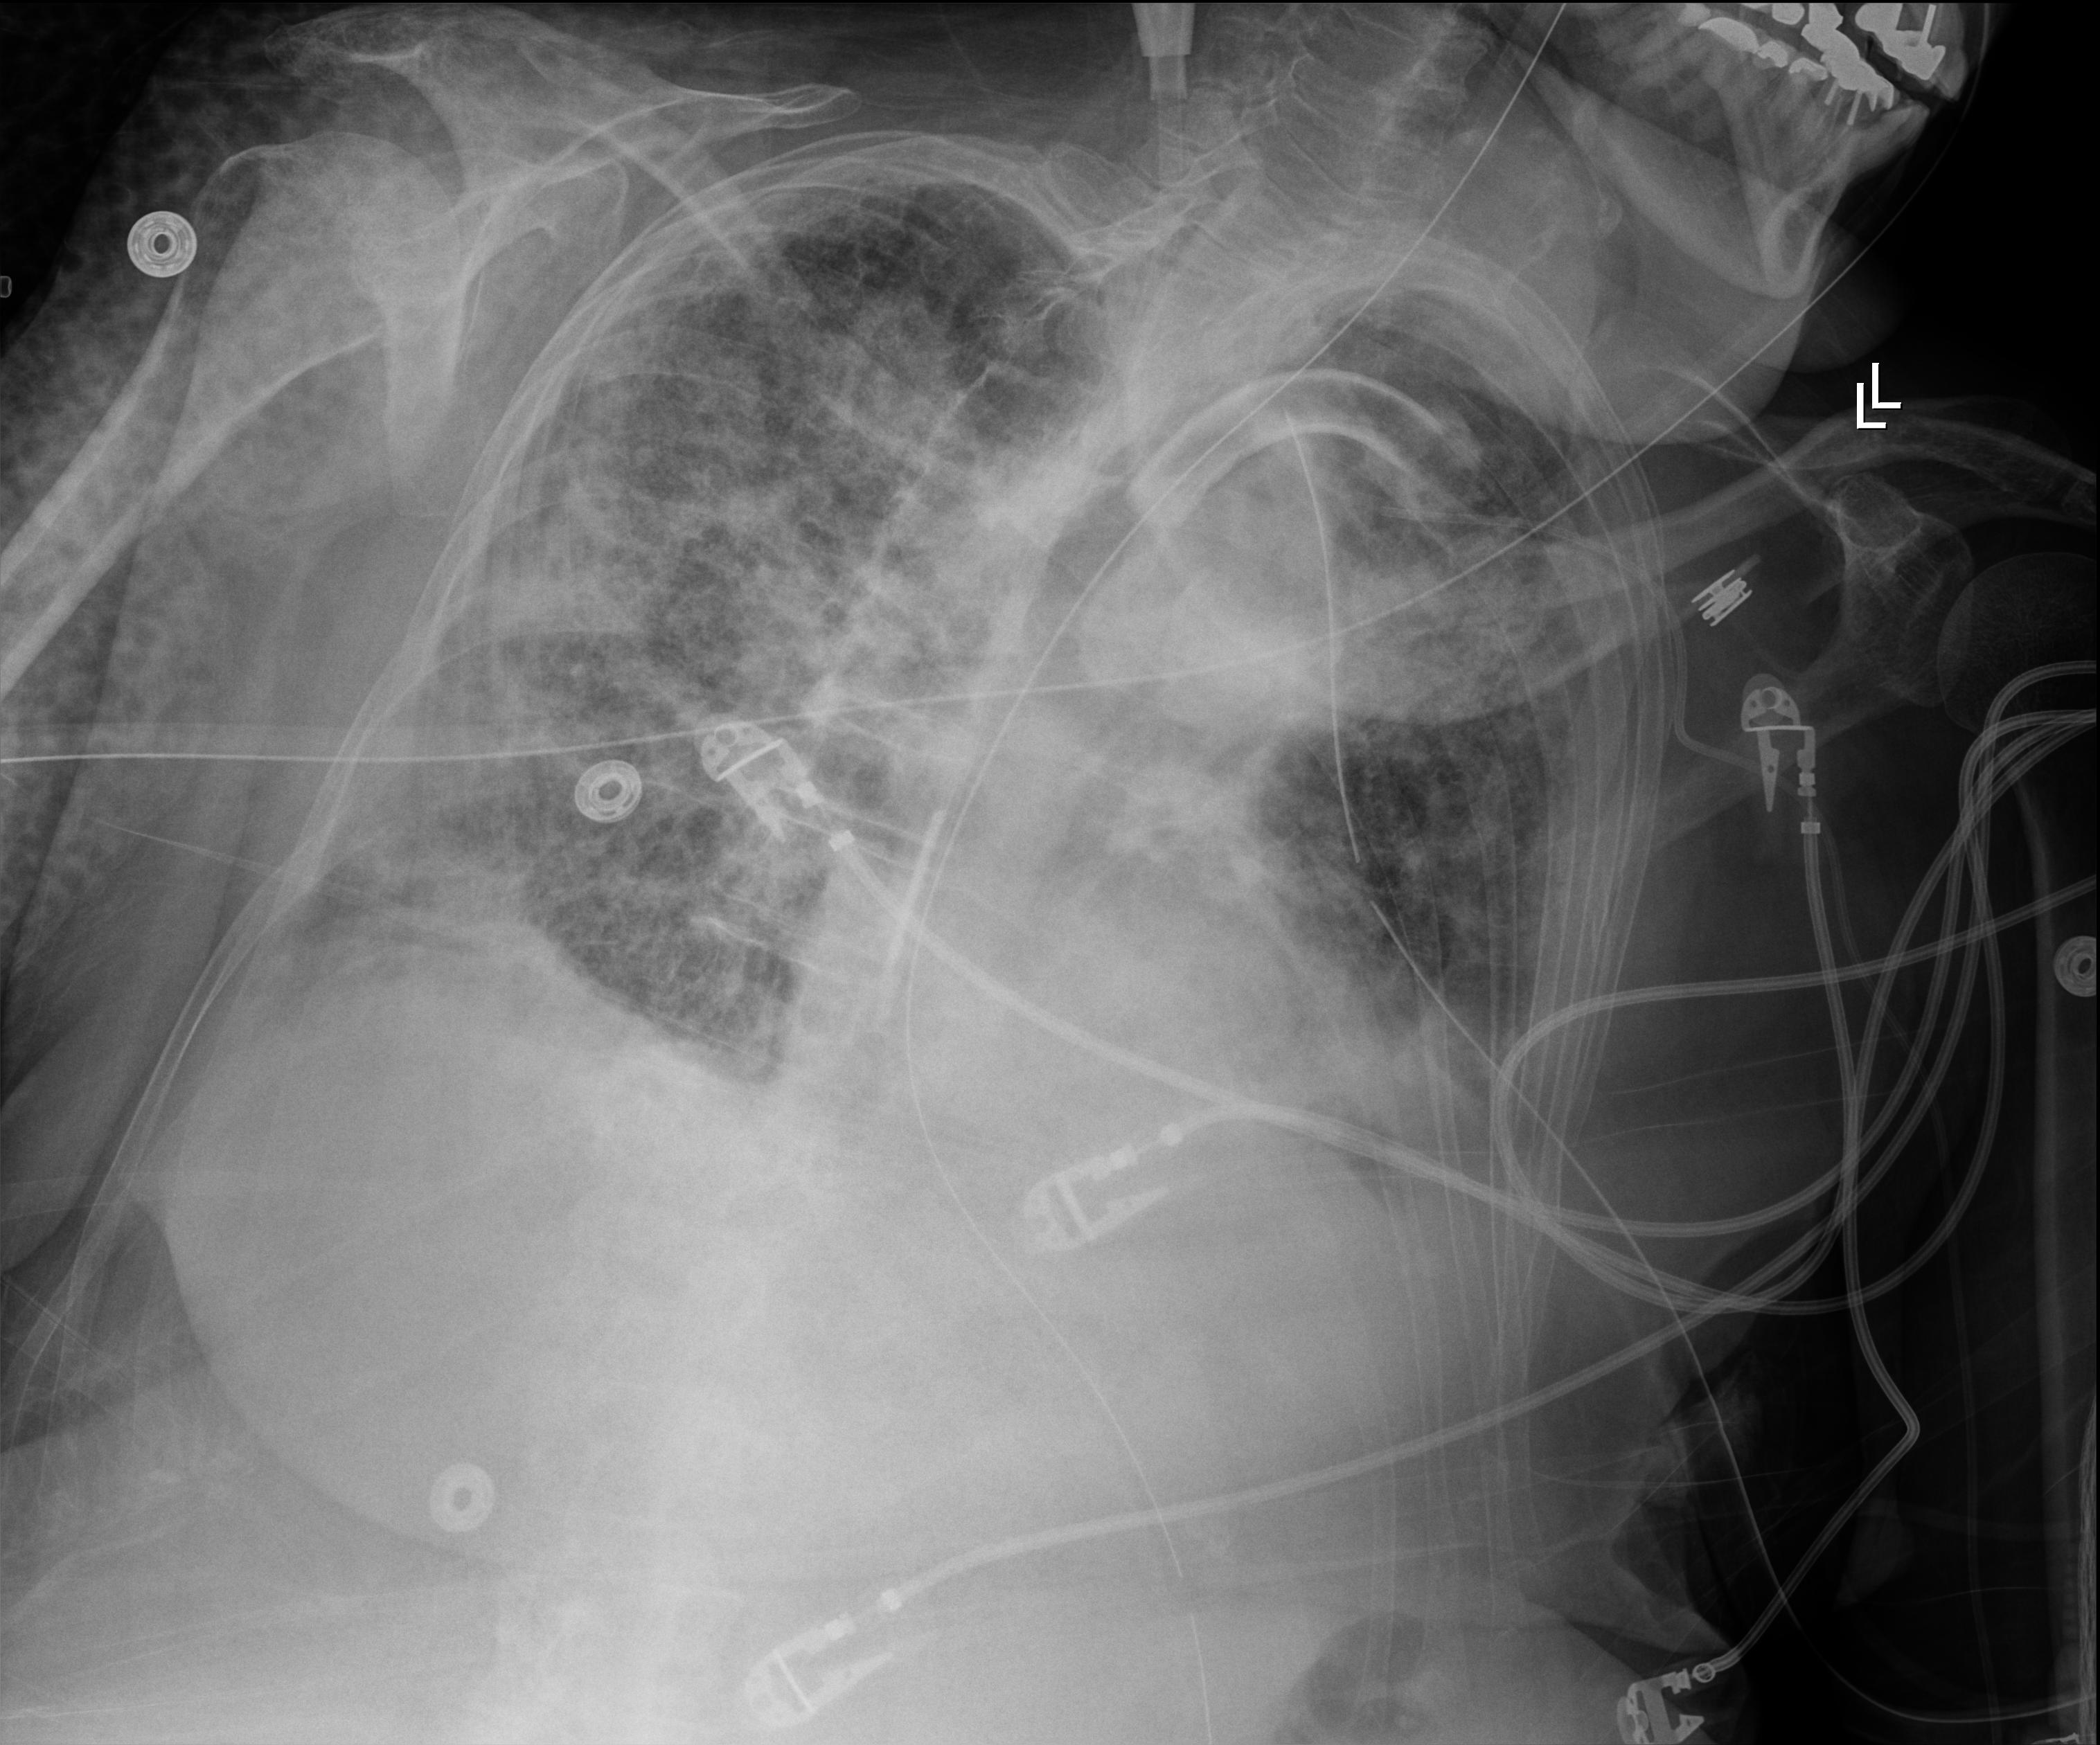
Chest X-ray (portable), anteroposterior (AP) projection. Female patient hospitalised with COVID-19, age 75–90 years.
From the hospital-stay record, not from the radiograph (when in the stay this image was taken is not recorded): admitted to intensive care during this hospital stay: yes; hypertension (admission record): yes.